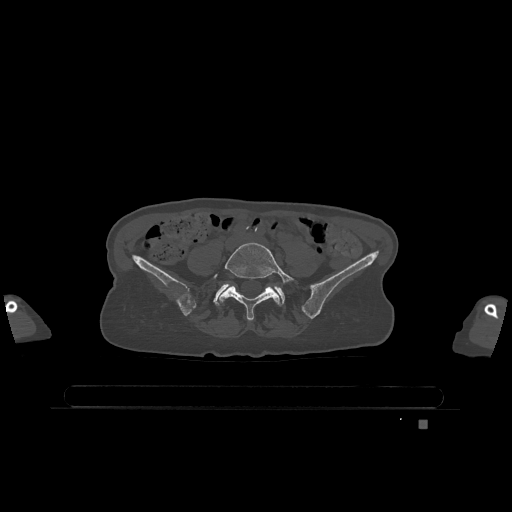
CT including the spine, one axial slice. Slice 235 of 1317 in the series (ordered by position). Bone window (W 1800 / L 400 HU). 512 × 512 image matrix, field of view 500 × 500 mm. Female patient, age 74 years. From the clinical record (not read from this slice): primary cancer: lung; vertebrae with lytic lesions (as recorded): T1, T4, T5, T6, L4, L5.
Outlined on this slice (semi-automatic segmentation, software-assisted and operator-edited):
- L5 vertebra: bounding box (x1, y1, x2, y2) in pixels: (214, 242, 294, 321)